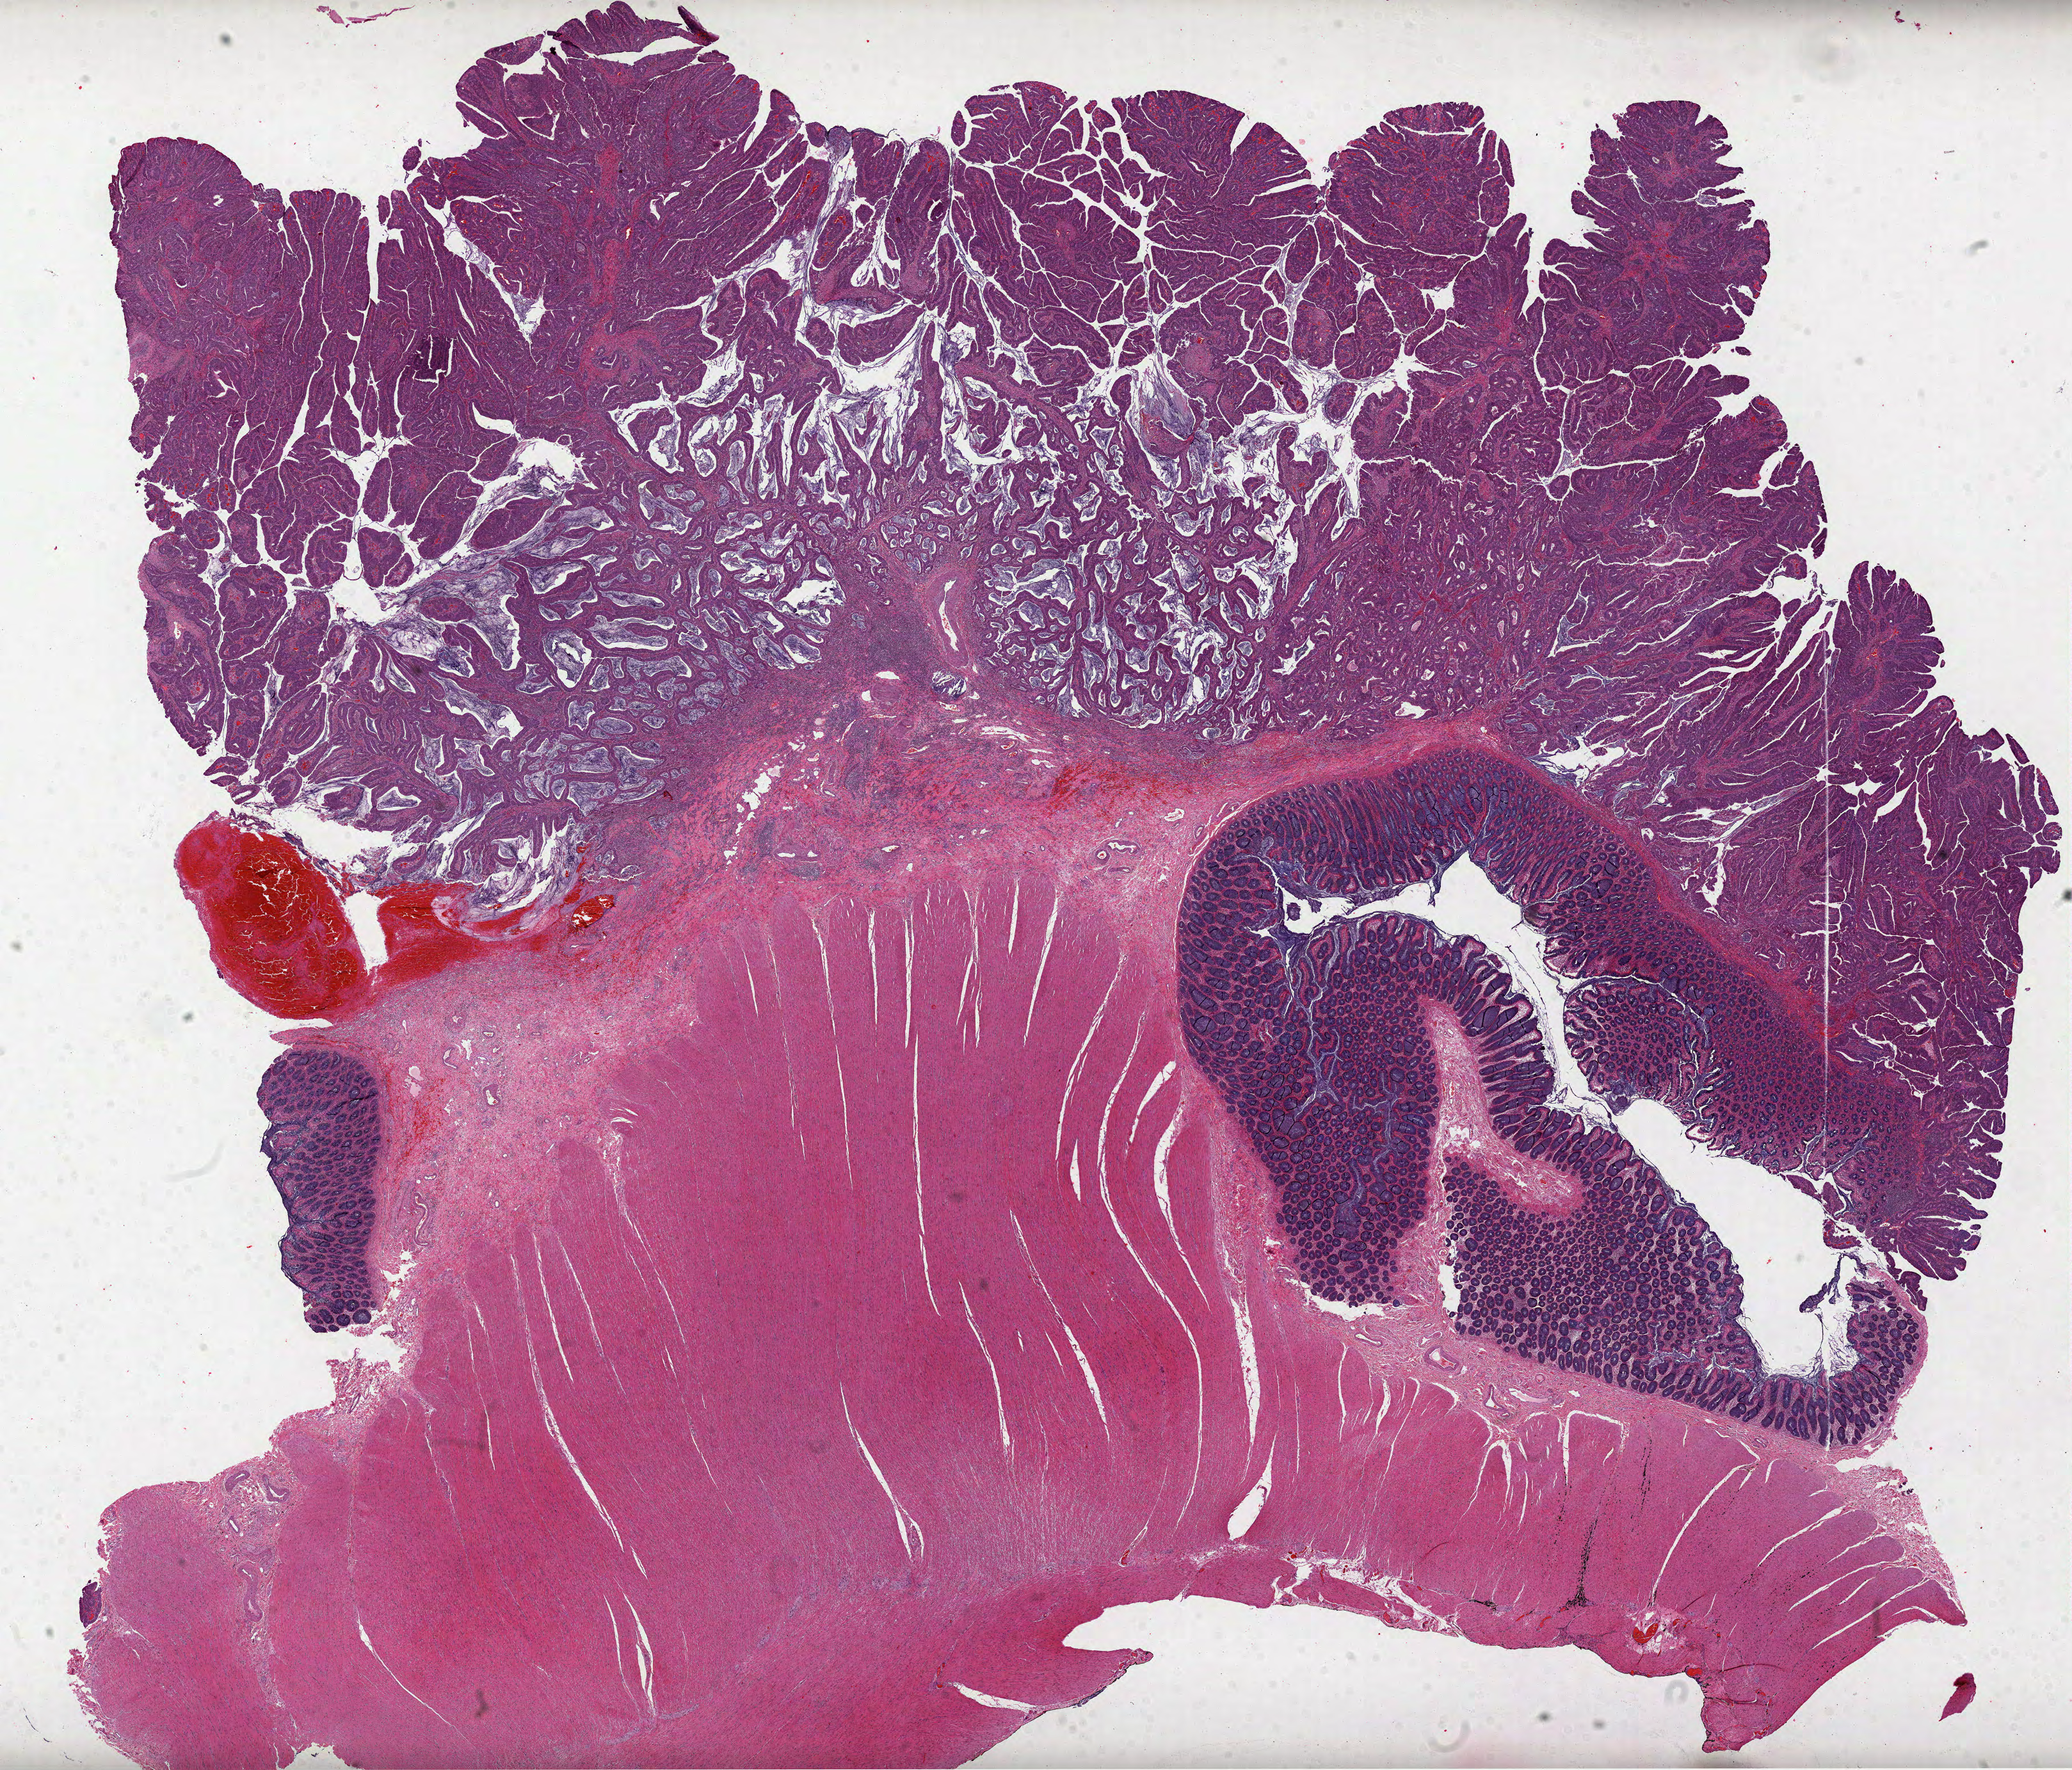
Whole-slide histology image, H&E-stained — whole scanned area (about 26.1 x 22.3 mm, from a 40x scan) shown as a low-resolution overview; formalin-fixed paraffin-embedded (FFPE) diagnostic section; sample: primary tumour, colon. Male, age 61 years at initial diagnosis.
• TNM: T2 N0 M0
• AJCC pathologic stage: I
• pathologic diagnosis: Adenocarcinoma, NOS (sigmoid colon)
• lymph nodes positive (case pathology): 0 of 17 examined